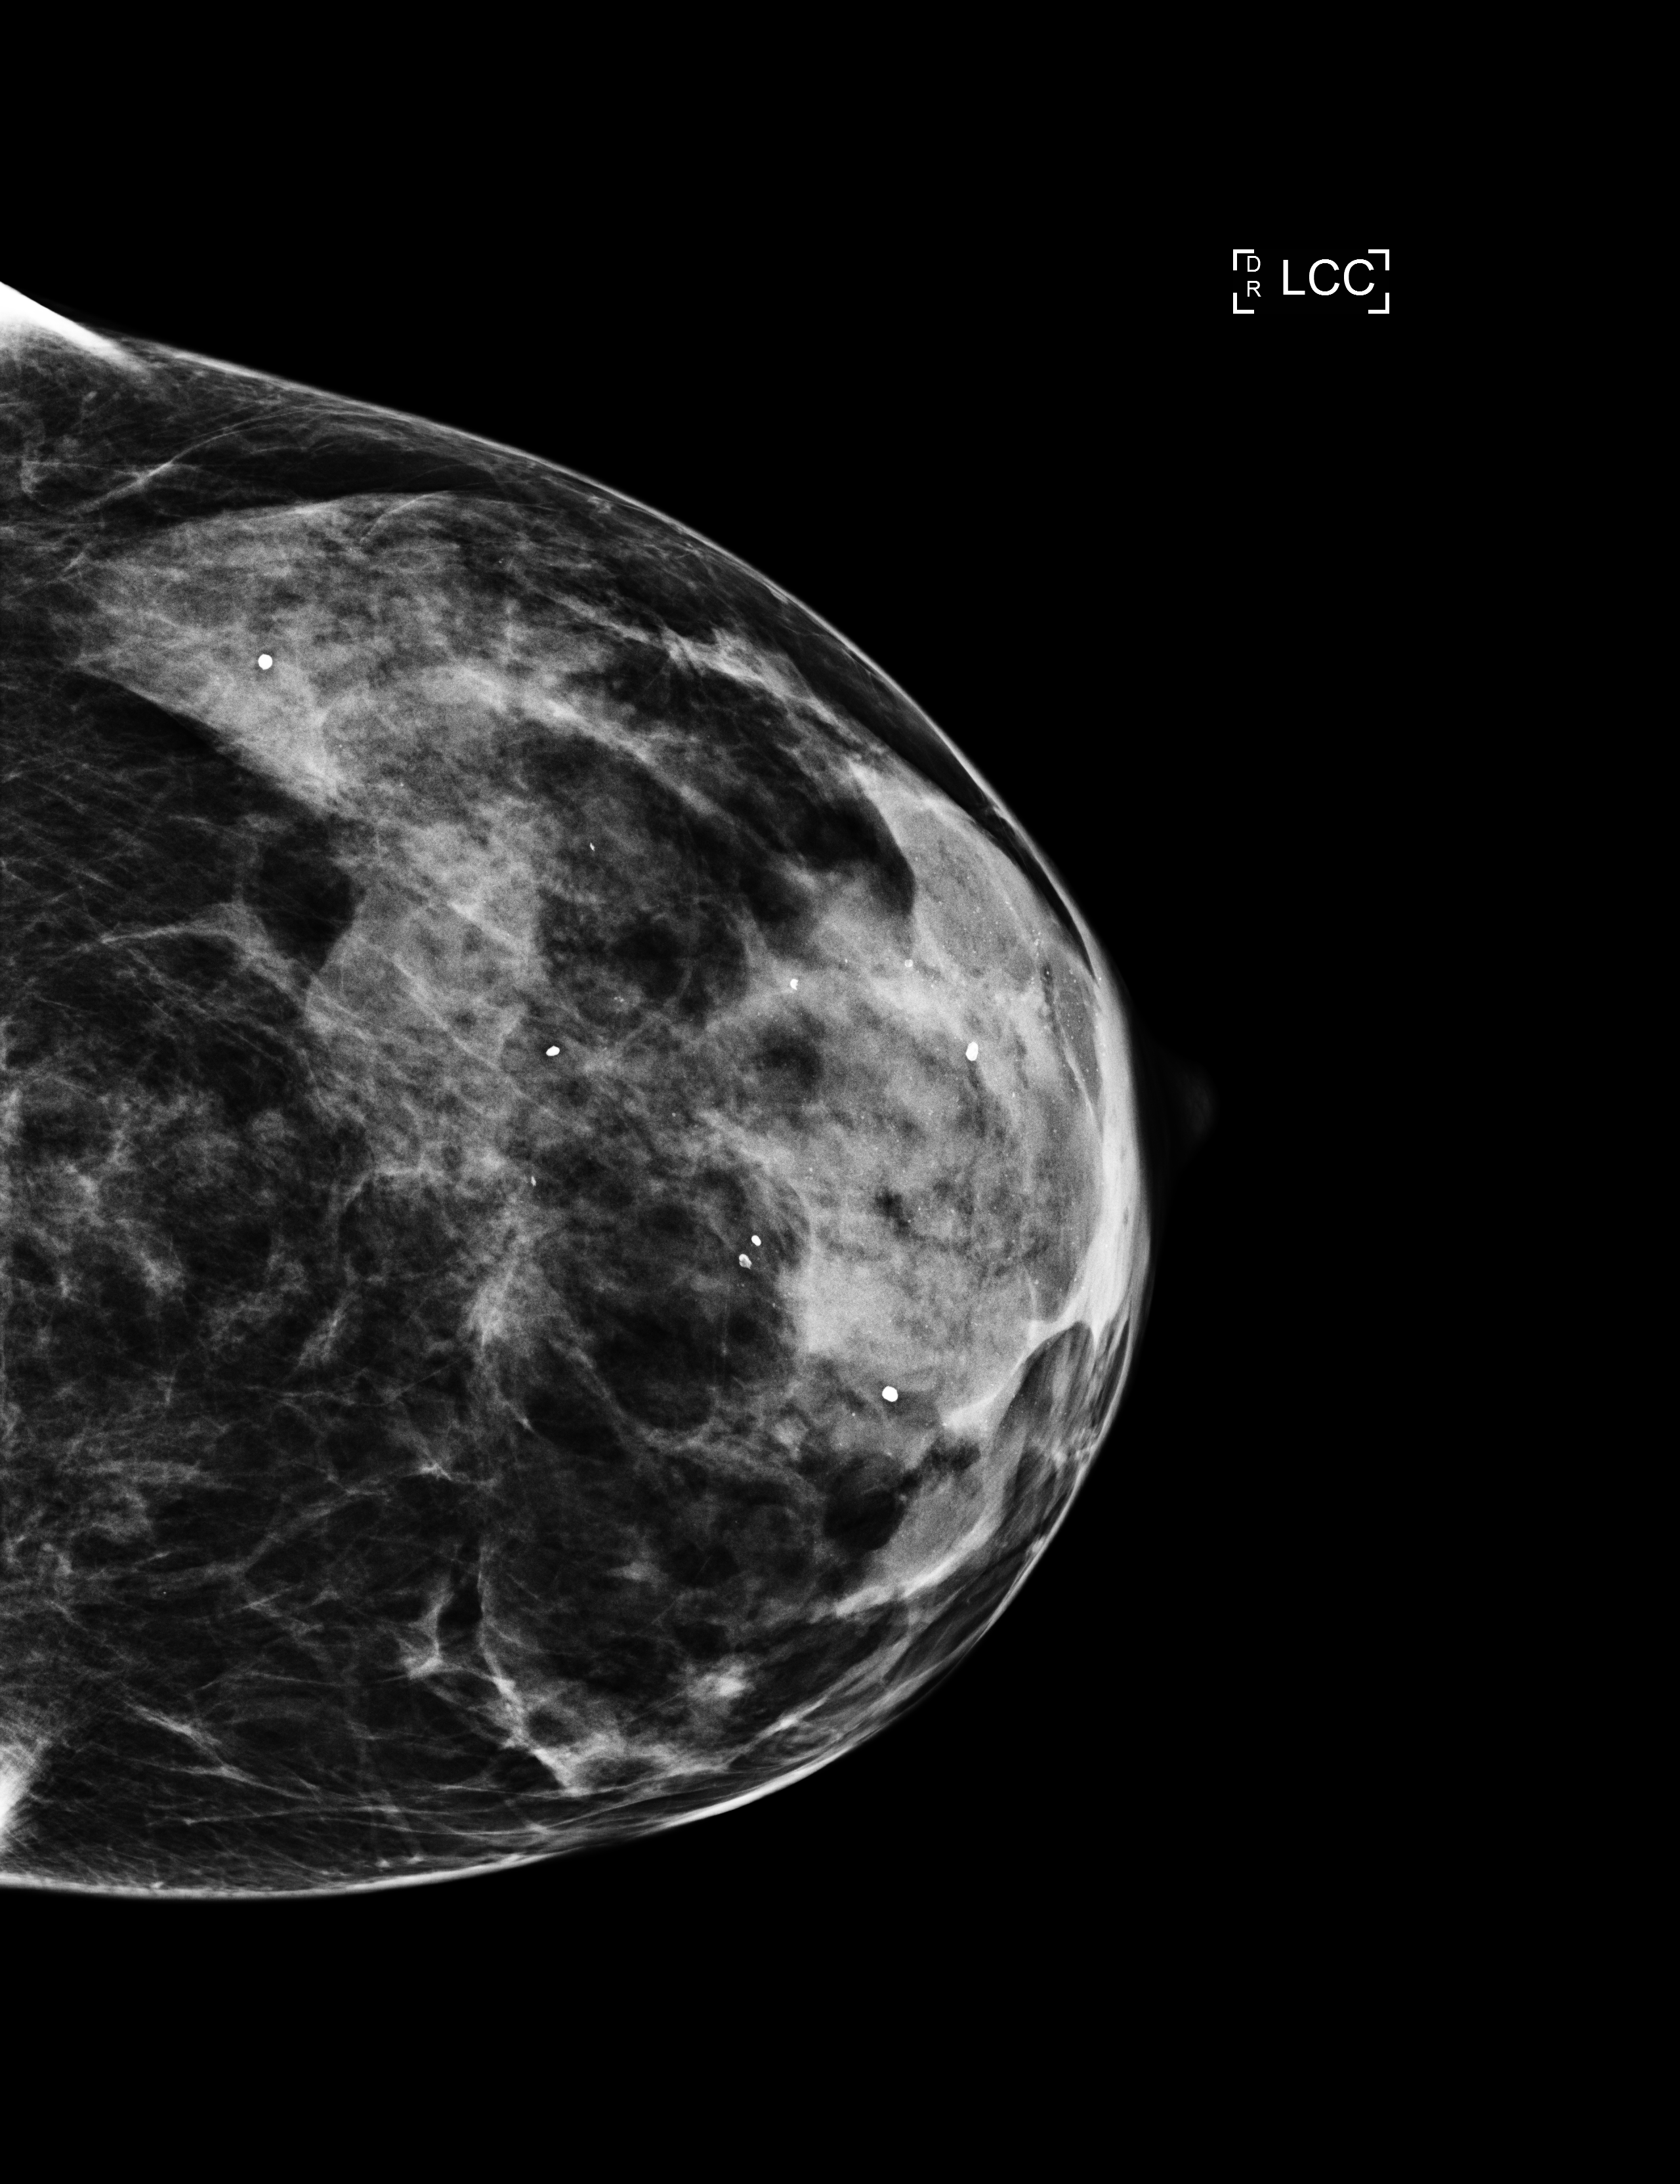
Screening examination. Patient aged 57 years (female).
Image type: full-field digital mammogram. Breast: left. Projection: CC view.